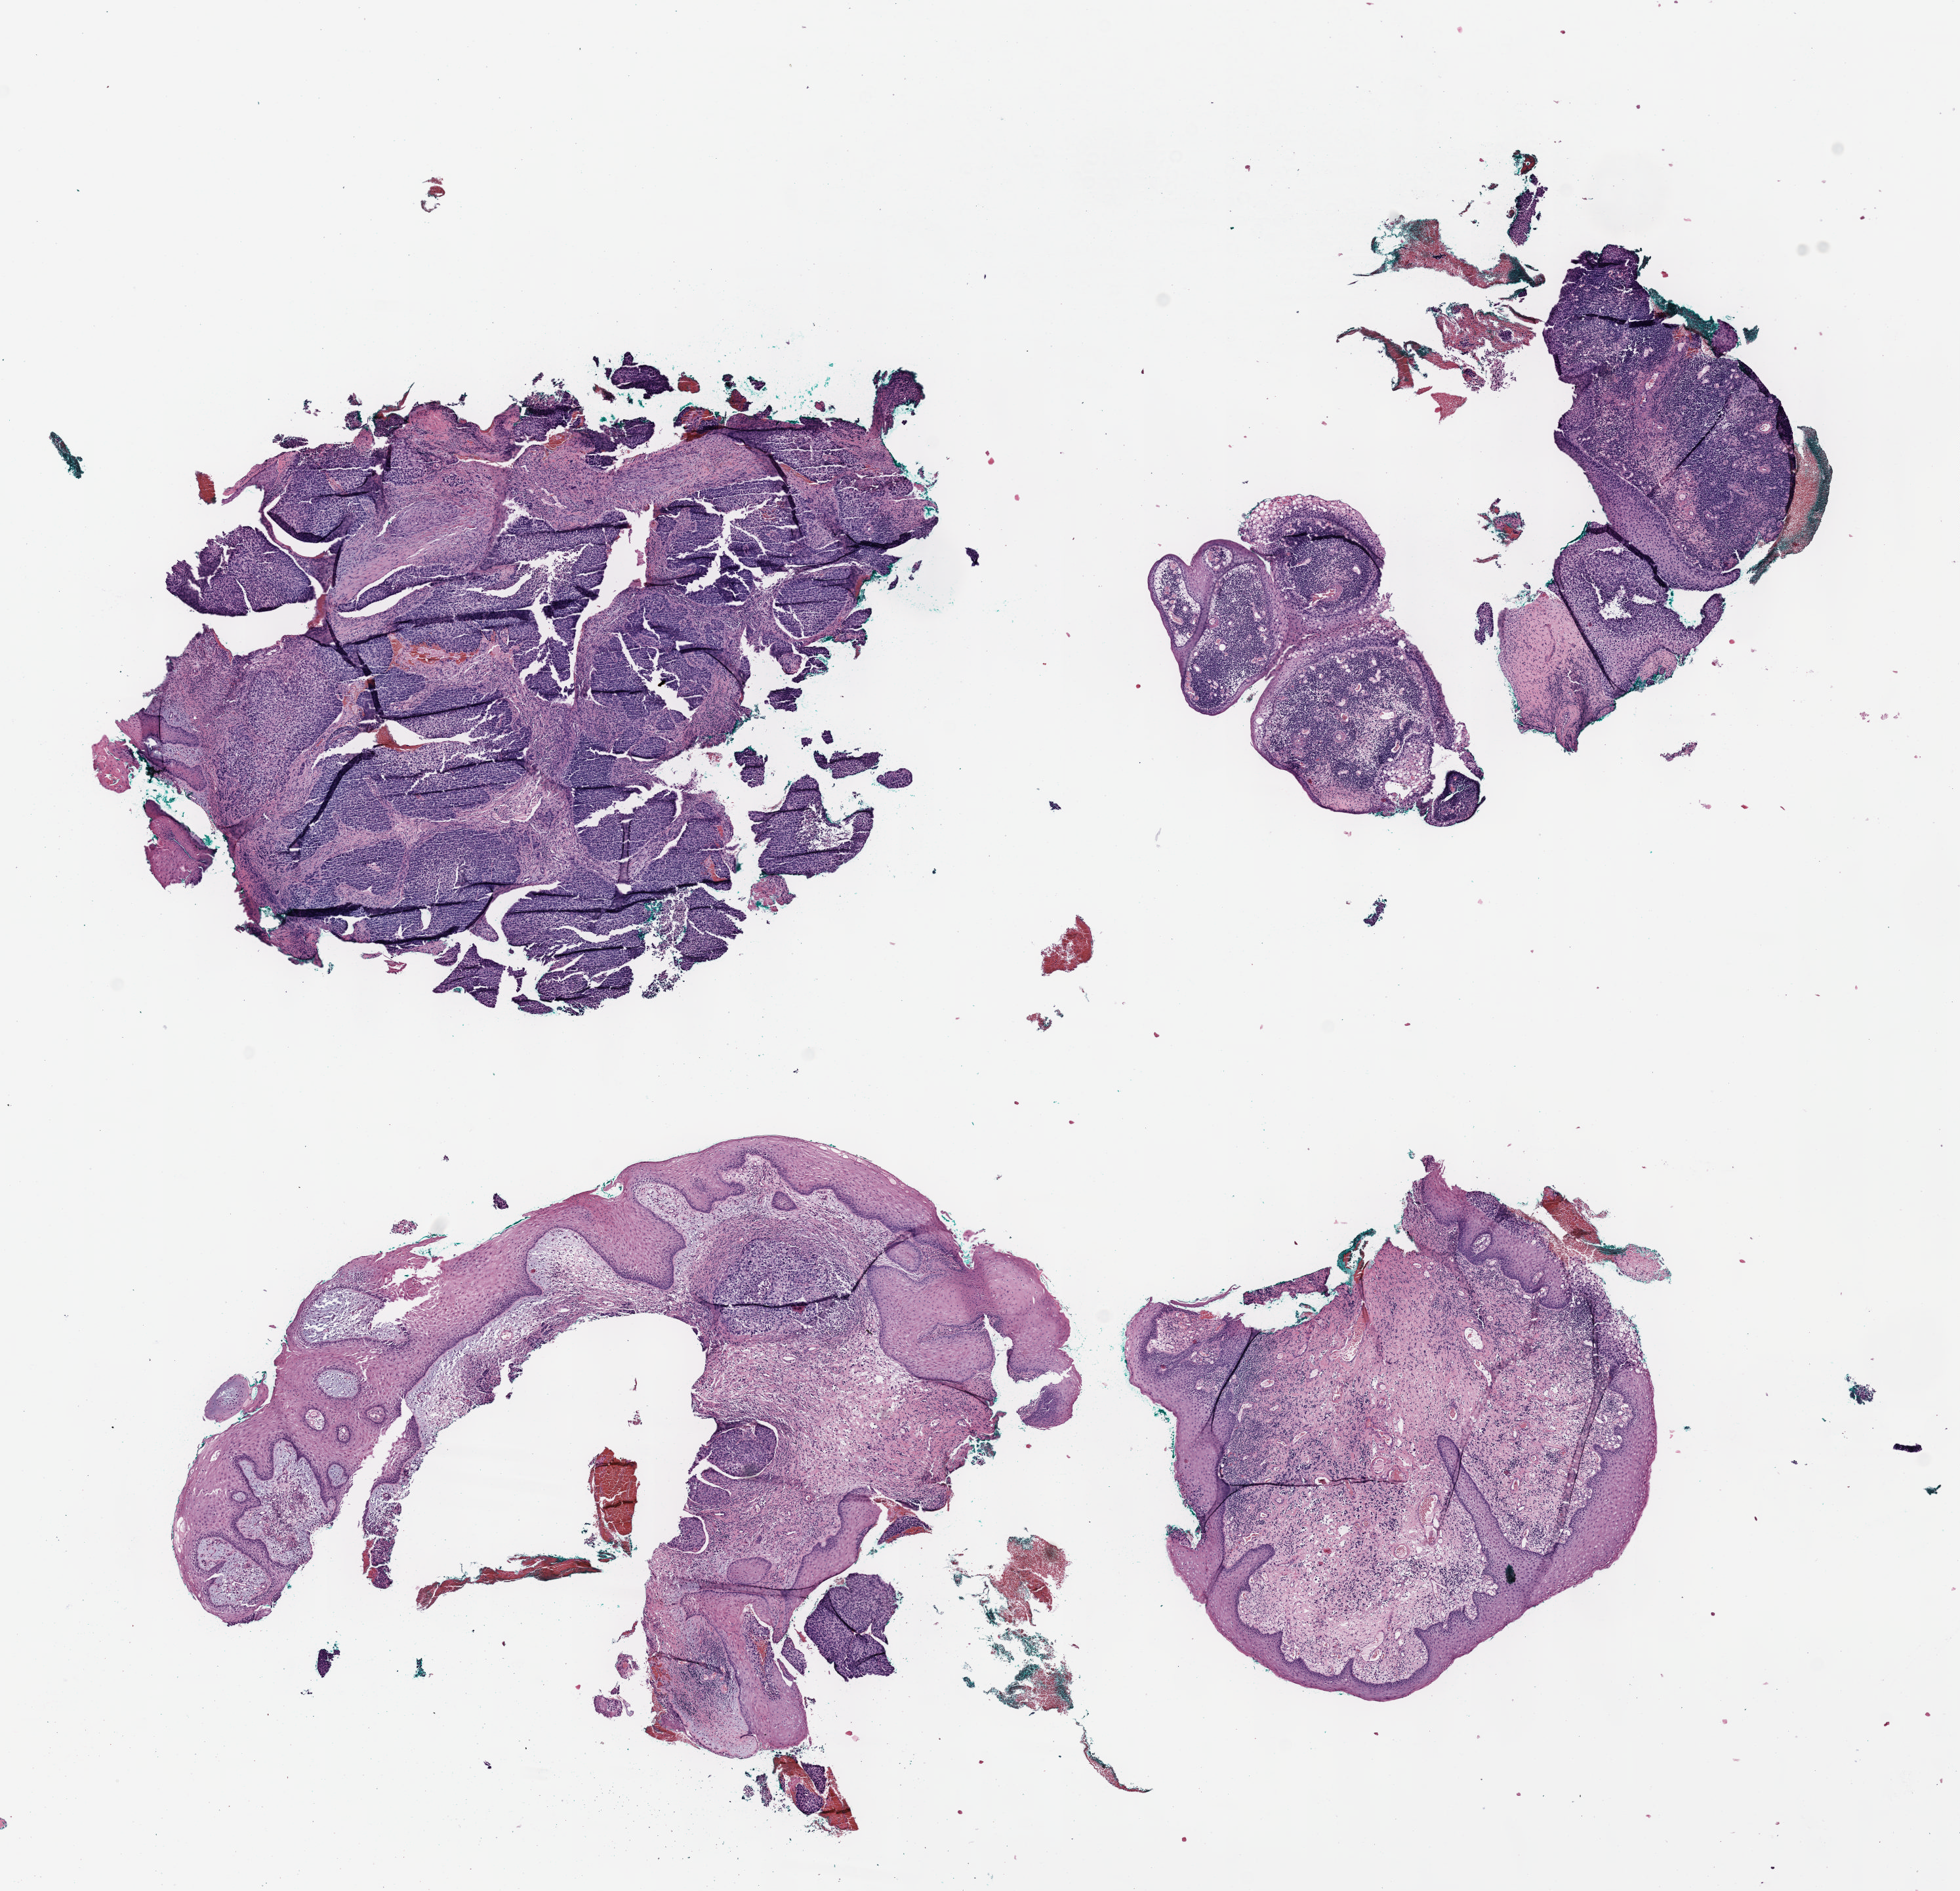
Digitized H&E tissue section (whole slide), shown as a low-resolution overview of the whole scanned area (about 12.1 x 11.6 mm, from a 40x scan), FFPE section, sample: primary tumour, cervix. Female patient; age at initial diagnosis 42 years. Histologic grade: G3 (poorly differentiated).
Pathologic diagnosis: Squamous cell carcinoma, NOS (cervix uteri). FIGO stage: IIIA.